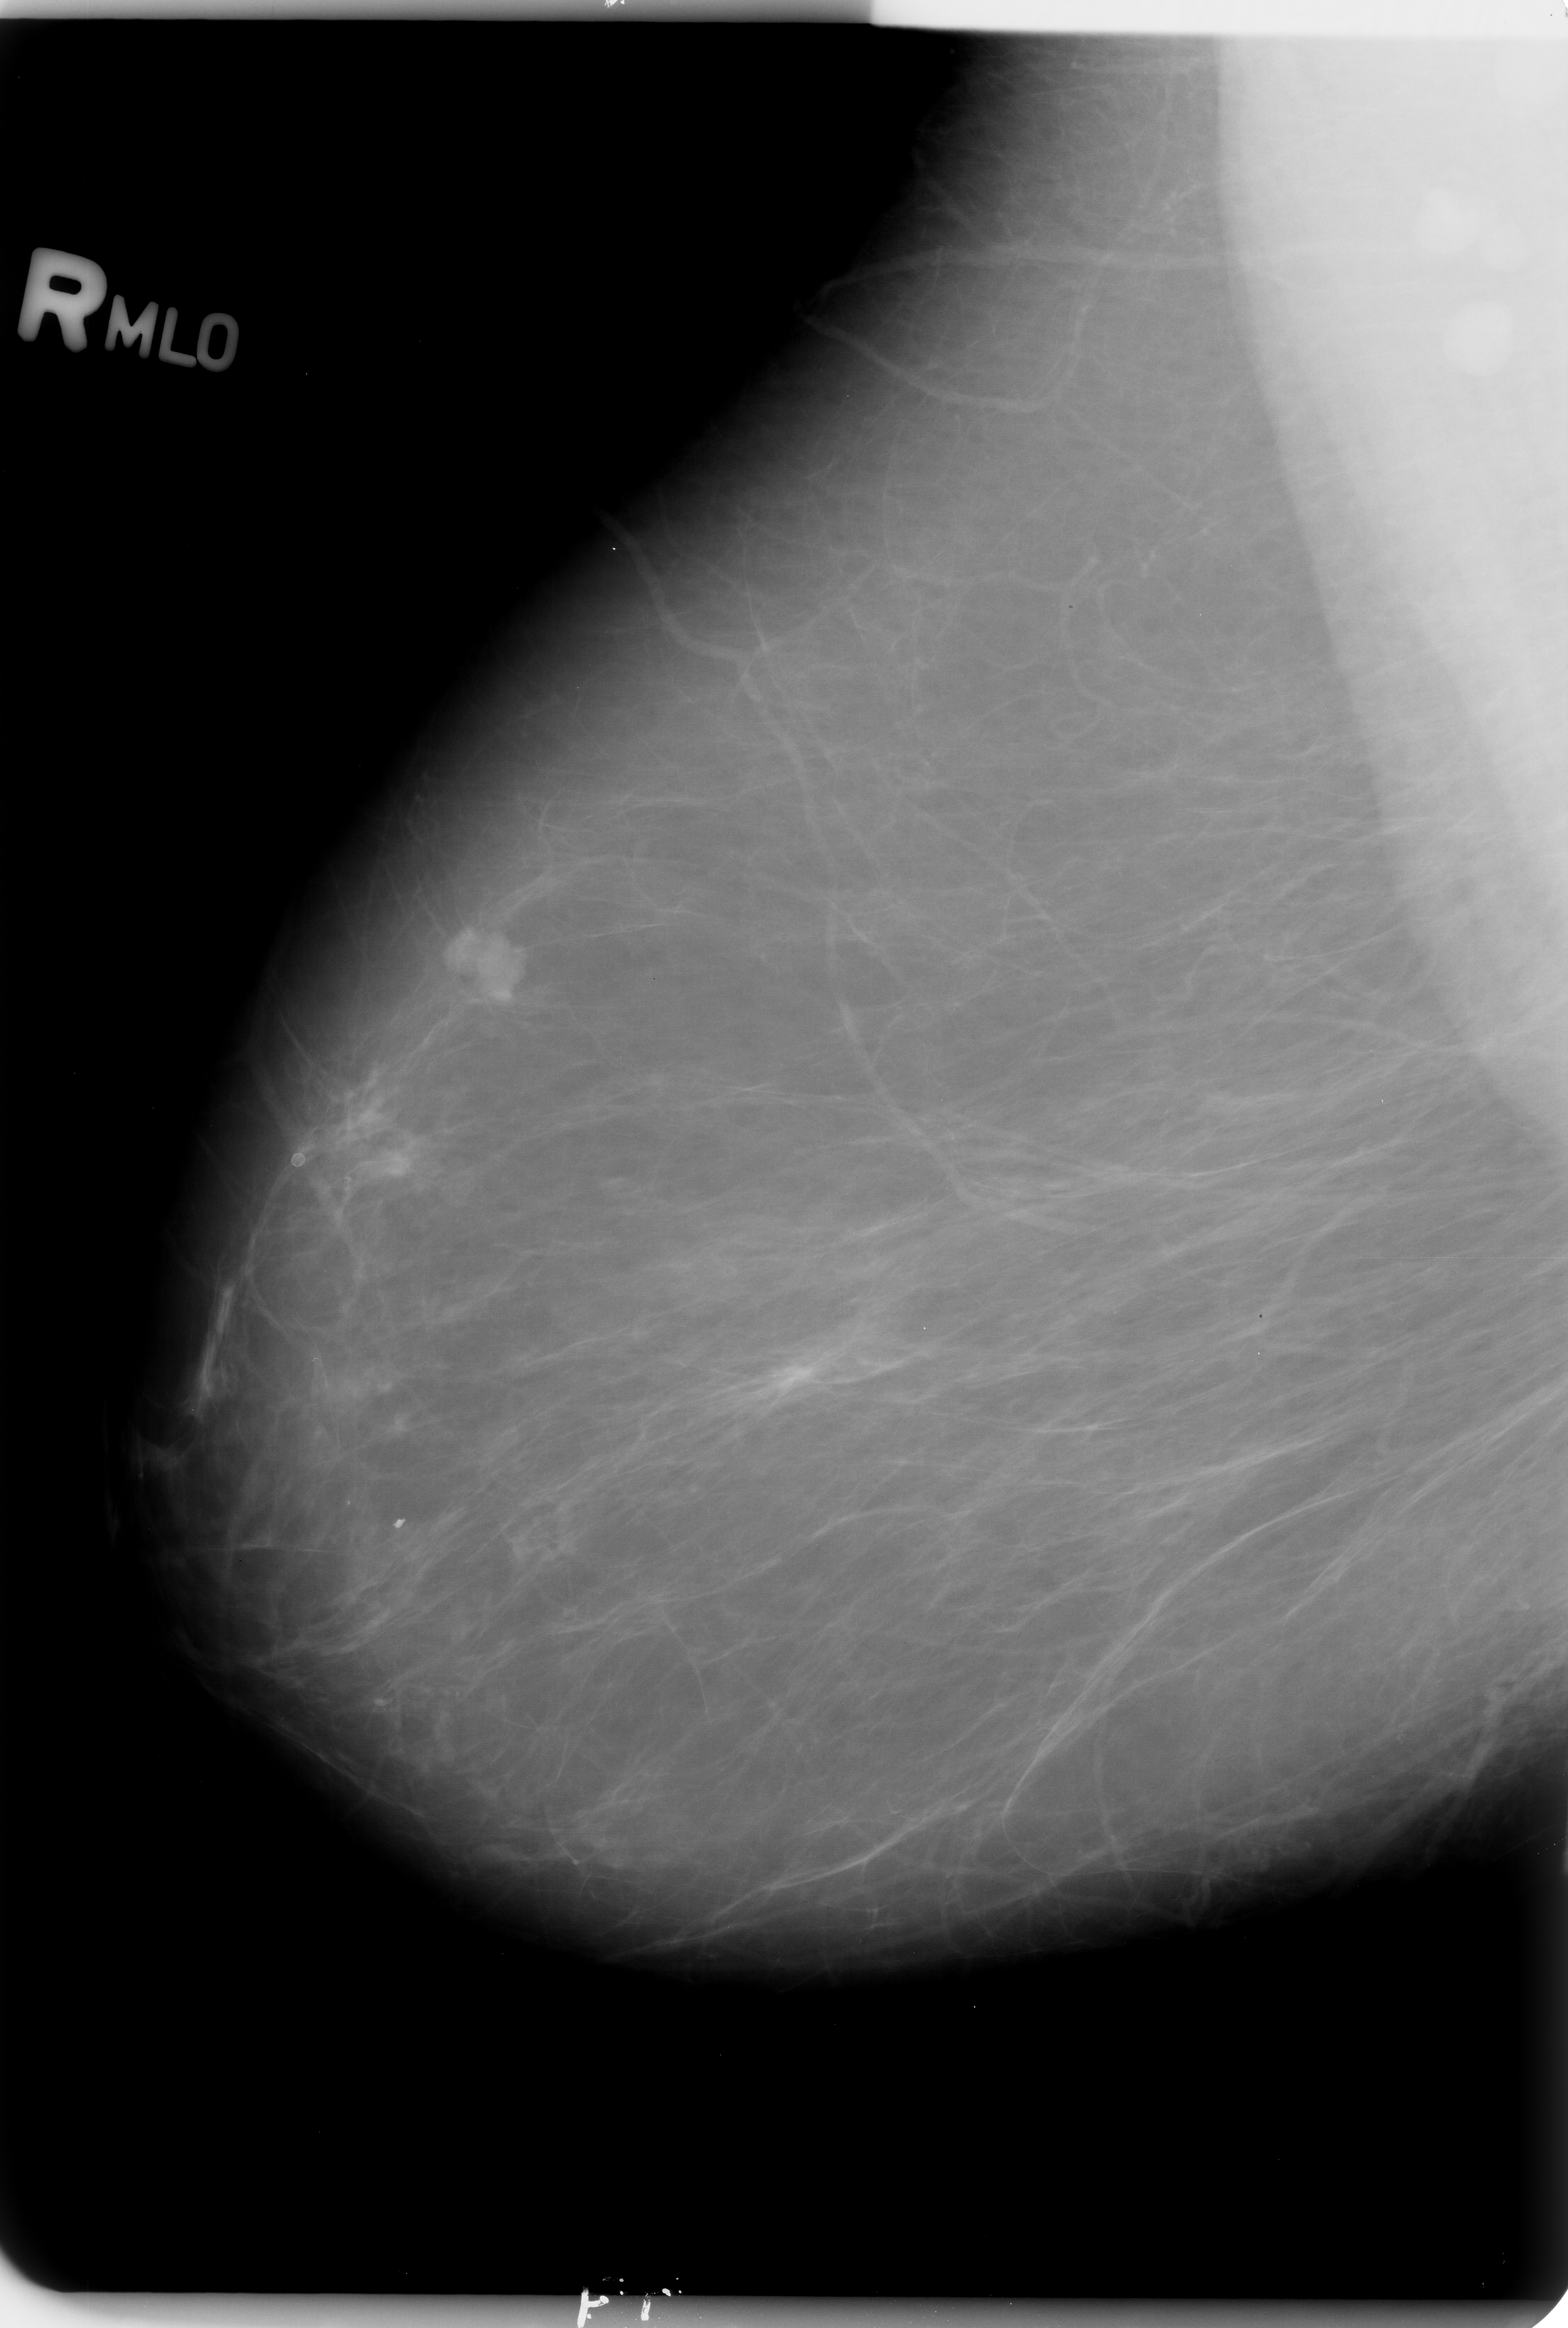
Digitized screen-film mammogram; right breast; mediolateral oblique (MLO) view; breast composition: almost entirely fatty (BI-RADS density category 1 of 4); 1568 × 2328 image matrix.
Expert-marked regions of interest on this film, with their recorded descriptors:
- mass, shape lobulated, margins circumscribed / ill defined; BI-RADS assessment category 4; subtlety rating 5 on a 1 (subtle) to 5 (obvious) scale; pathology (as recorded): benign: bounding box <439,927,530,1012> (left, top, right, bottom; pixels)